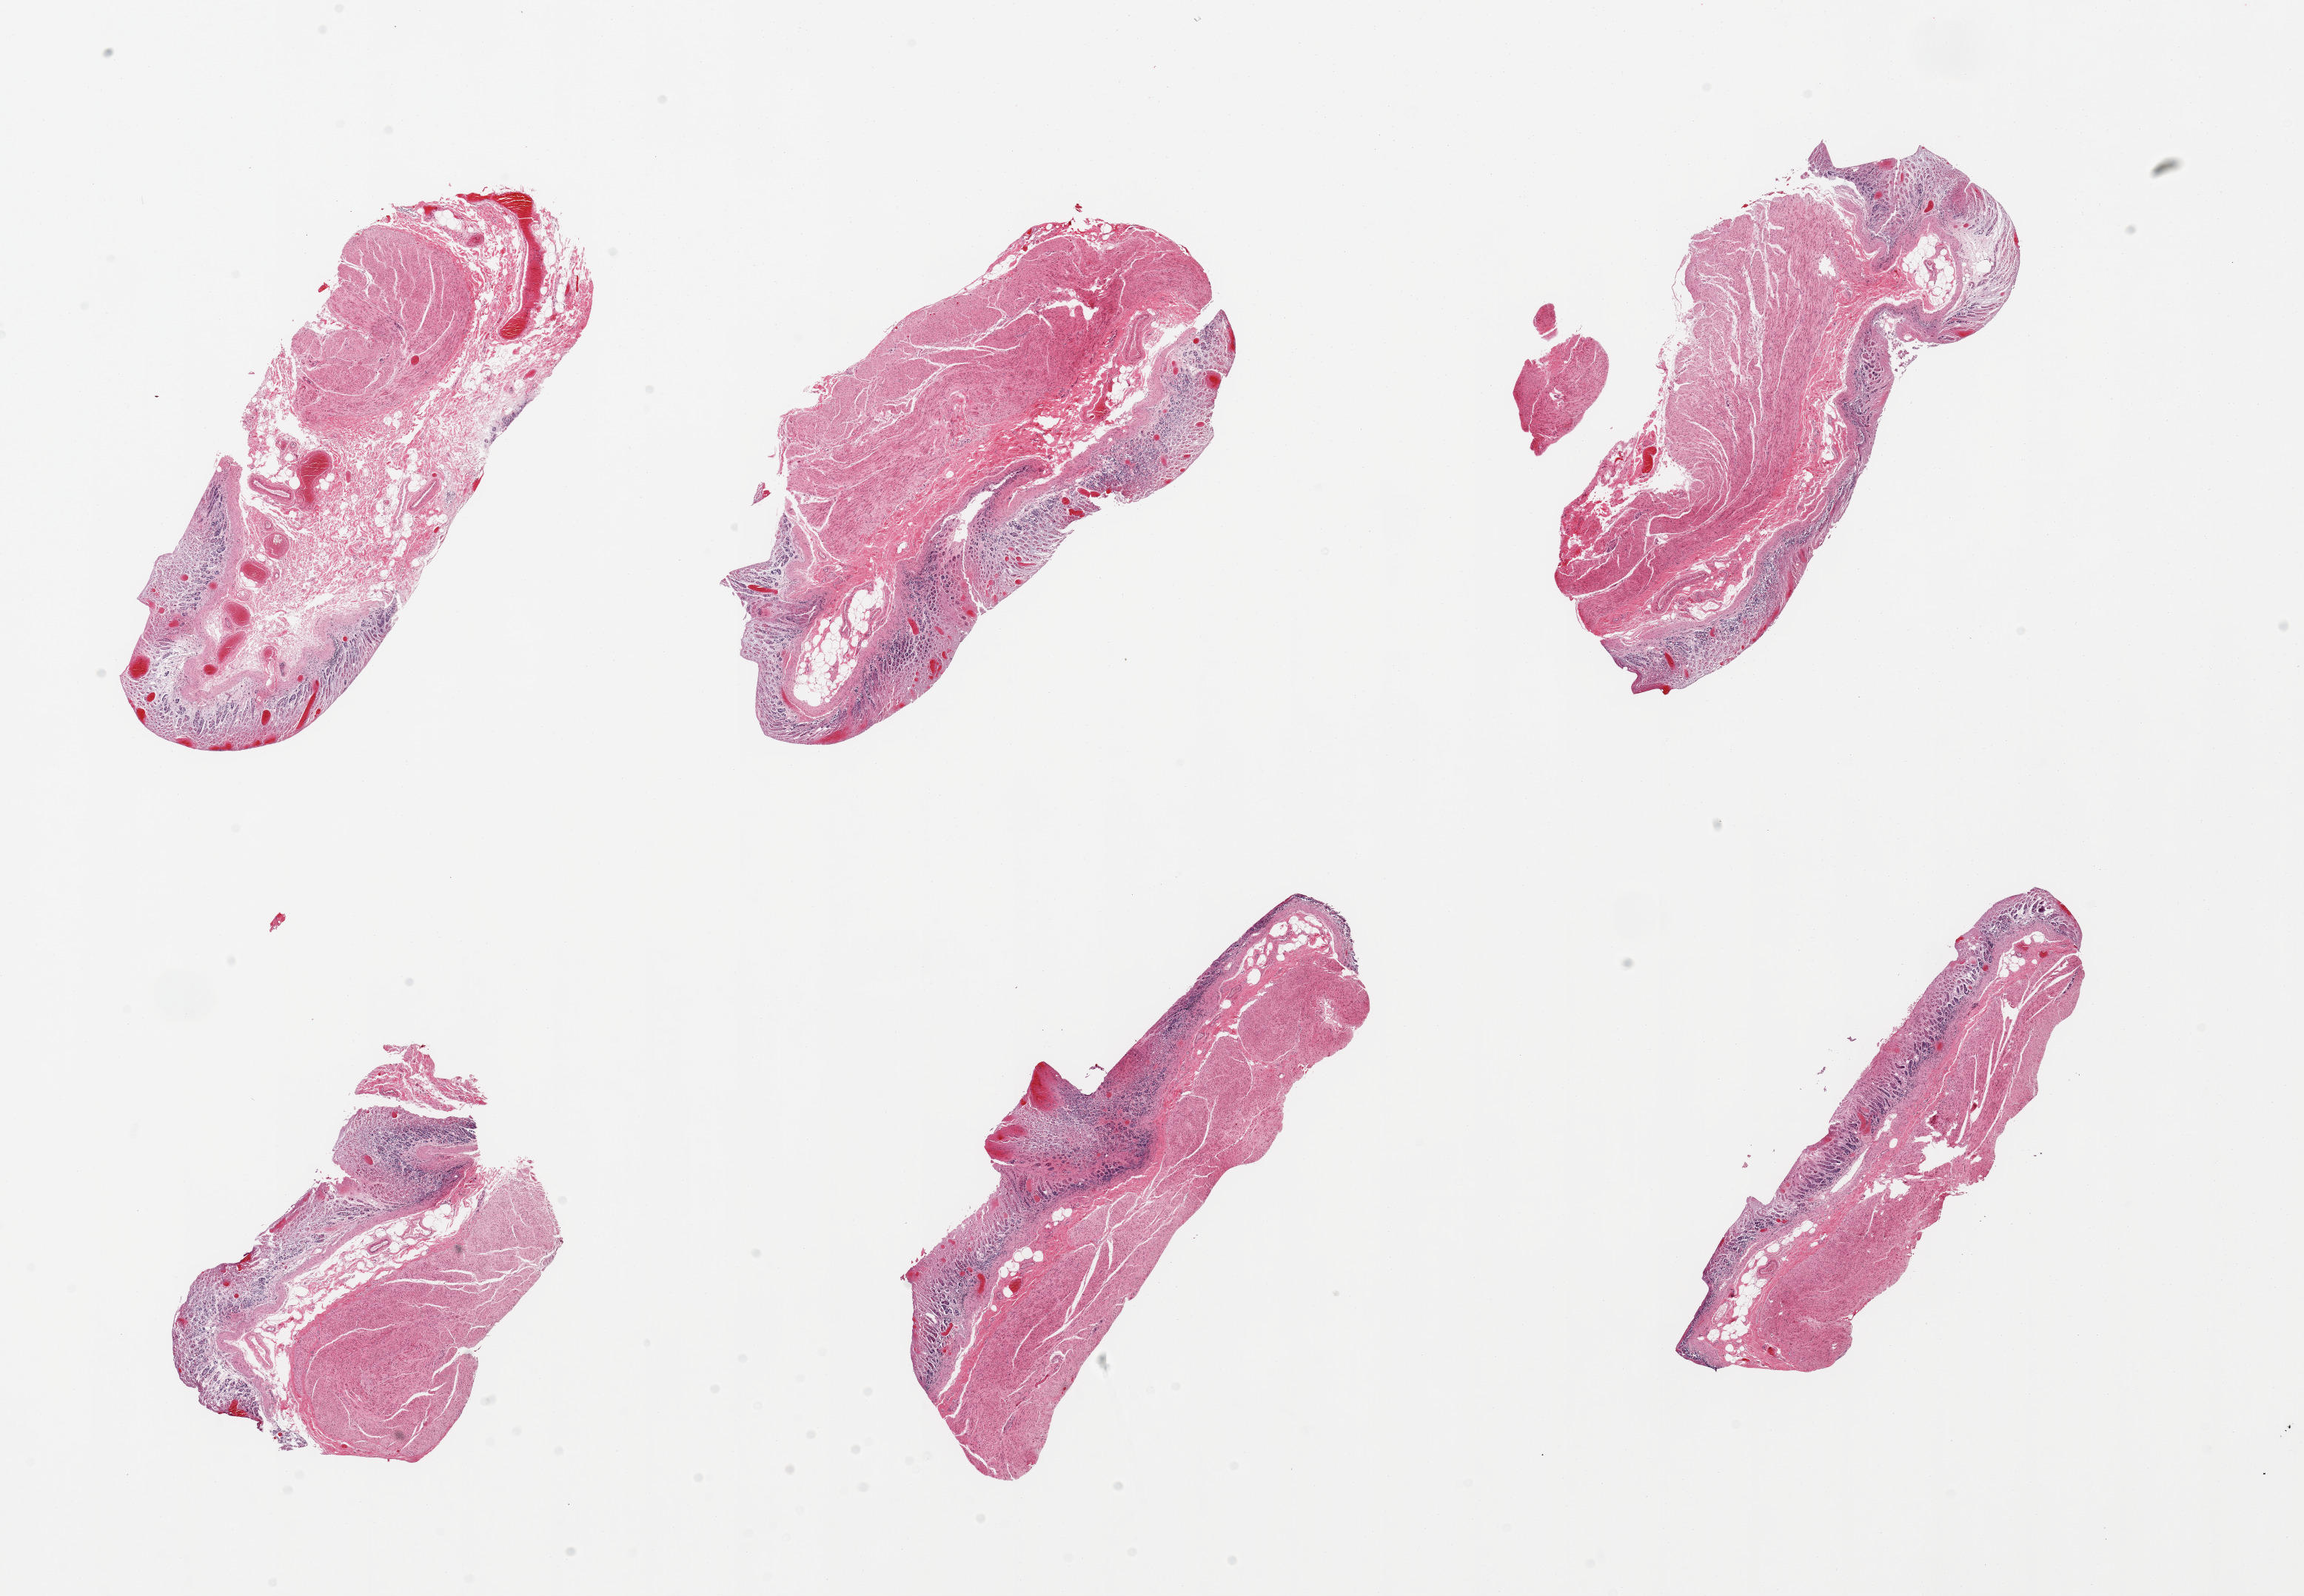
Digitized hematoxylin and eosin (H&E)-stained section, low-resolution overview of the scanned area, about 24.6 x 17.1 mm, PAXgene-fixed paraffin-embedded (PFPE) section, target tissue: stomach, tissue donor sample. Female donor.
• reviewer comment on this tissue sample: 6 pieces; full thickness sections with moderately to severely autolyzed mucosa